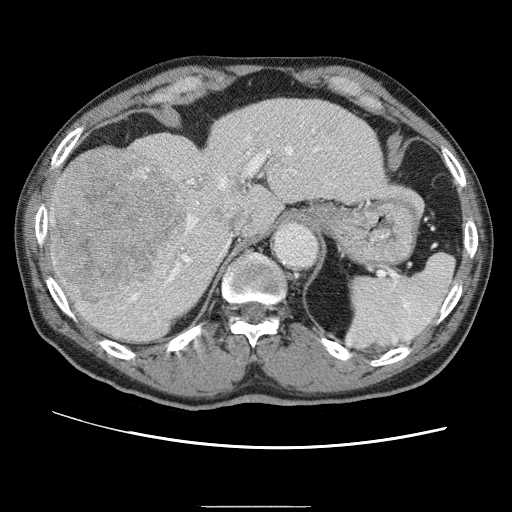
Contrast-enhanced abdominal CT (liver protocol), one axial slice; position 42 of 75 along the scan axis; reconstruction kernel STANDARD; 120 kVp; one of 2 acquisitions stored at this slice position; soft-tissue window (W 400 / L 40 HU); 2.5 mm slice thickness; 512 × 512 image matrix, field of view 360 × 360 mm. From the clinical record (not read from this slice): diagnosis: hepatocellular carcinoma (patient treated with transarterial chemoembolisation; whether this scan precedes or follows treatment is not stated here); TNM stage (as recorded): Stage-II; Child-Pugh class: A; tumour differentiation: well differentiated; tumour size: 2 cm.
Annotated regions visible in this slice (semi-automatically segmented with operator editing):
- liver parenchyma outside the tumour (the mass and vessels are separate outlines, so this box may not span the whole liver): box from (x=50, y=98) to (x=394, y=342) px
- mass: (x=49, y=151)–(x=181, y=297)
- liver vessels: (x=80, y=134)–(x=315, y=311)